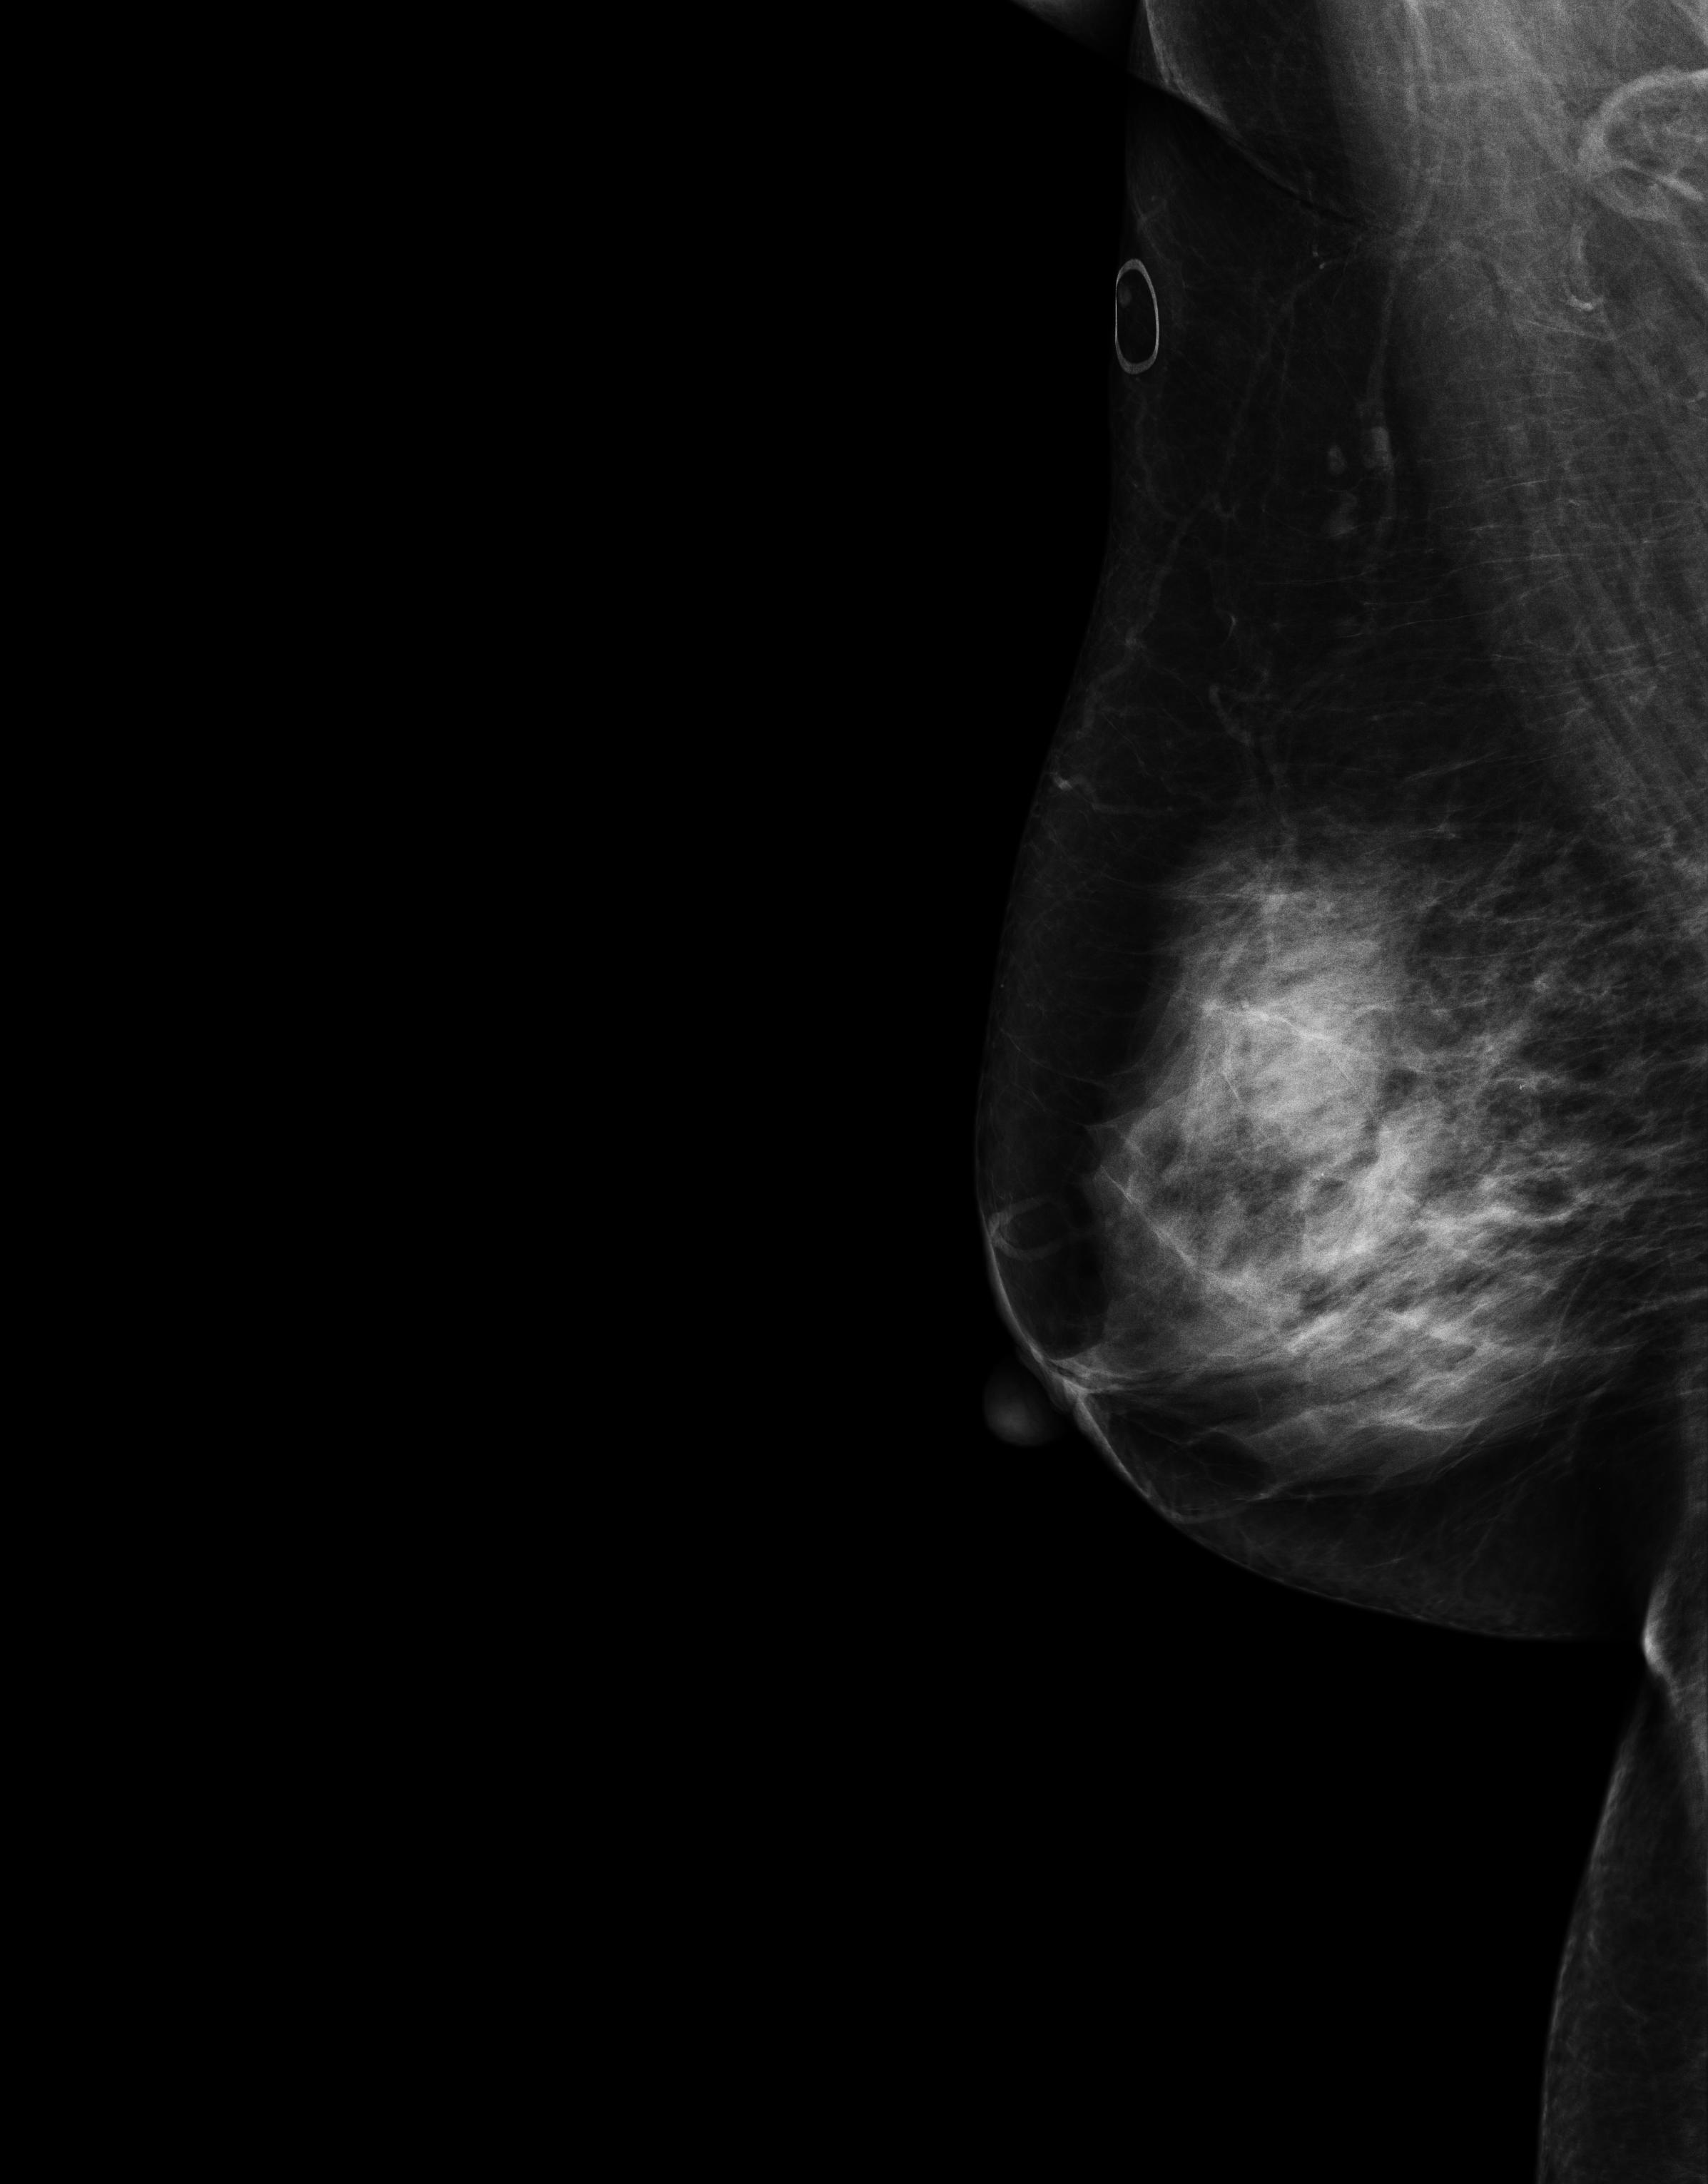
Digital mammogram (FFDM); right breast; mediolateral oblique (MLO) view; annual screening mammography examination; compressed breast thickness 65 mm; system: Senographe Essential ADS_56.21.3. Patient: female, 67 years.
BI-RADS breast density category at the screening exam (both breasts, scale 1–4): 3. Final BI-RADS category for the screening round (tomosynthesis exam, both breasts): category 1. Recall: no recall after this screen.